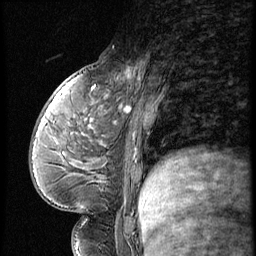
Breast MRI (dynamic contrast-enhanced), one sagittal slice; slice 25 of 56 in the series (ordered by position); 3 images stored at this slice position (order not interpretable as contrast timing); 1.5 T; TE 4.2 ms, TR 9 ms; 2.5 mm slice thickness; 256 × 256 image matrix. Patient: female, 54 years. From the clinical record (not read from this slice): setting: breast cancer imaged before/during neoadjuvant chemotherapy; receptor status: triple-negative.
Structures marked on this image (semi-automatic segmentation, software-assisted and operator-edited):
- analysis volume of interest (the breast-tissue region the enhancement analysis was run in; not a lesion): box from (x=99, y=53) to (x=149, y=102) px
- tumour enhancement mask (voxels above the 140 % enhancement threshold inside the analysis volume of interest): (x=120, y=67)–(x=137, y=82)